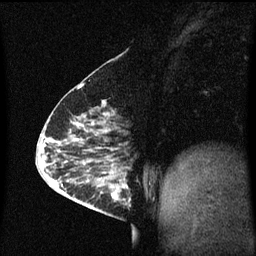
Breast MRI (dynamic contrast-enhanced), one sagittal slice; slice 25 of 60 in the series (ordered by position); dynamic contrast-enhanced series, image 2 of 3 at this slice position (ordered by acquisition); 1.5 T; TE 4.2 ms, TR 8.4 ms; 256 × 256 image matrix, field of view 200 × 200 mm. Patient: female, 63 years.
Outlined on this slice (semi-automatic segmentation, software-assisted and operator-edited):
- analysis volume of interest (the breast-tissue region the enhancement analysis was run in; not a lesion): bounding box (x1, y1, x2, y2) in pixels: (98, 168, 133, 217)
- tumour enhancement mask (voxels above the 70 % enhancement threshold inside the analysis volume of interest): (100, 170, 129, 201)